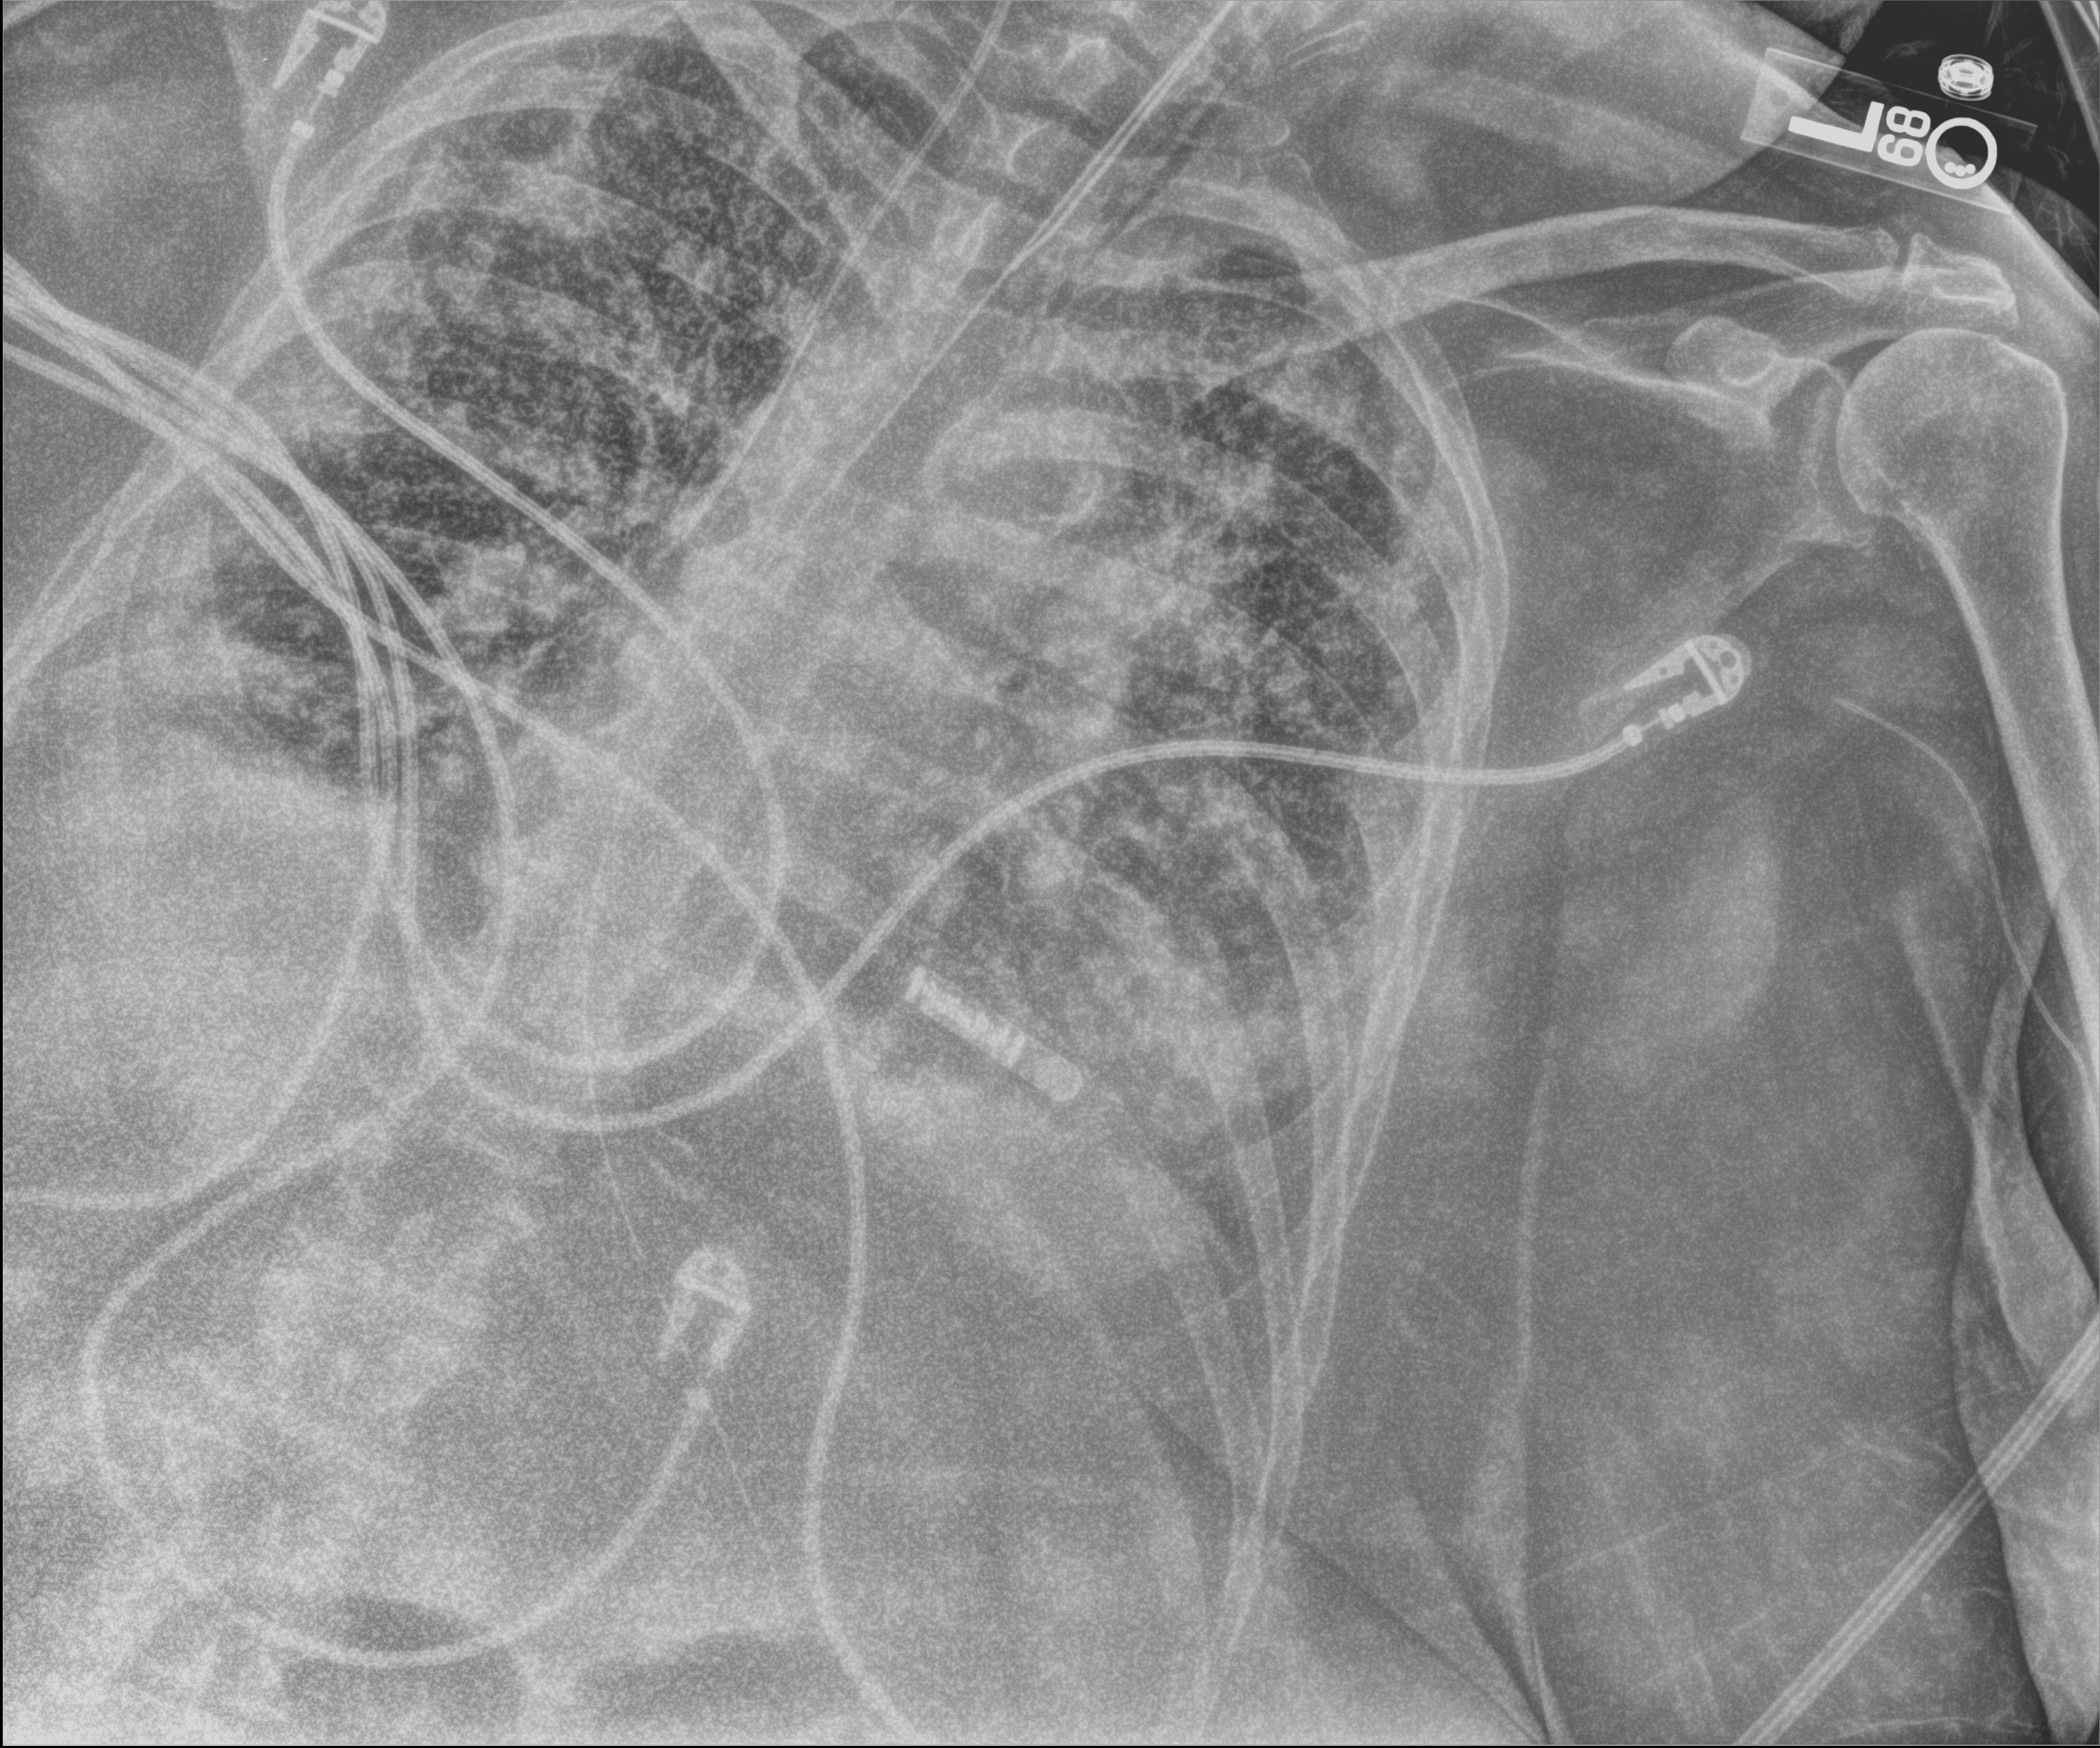
Bedside chest radiograph (computed radiography); anteroposterior (AP) projection. Patient hospitalised with COVID-19; female, aged 60–74 years.
Admission-level facts for this patient (not findings on this image; timing relative to this image not recorded): other chronic lung disease (admission record): yes.